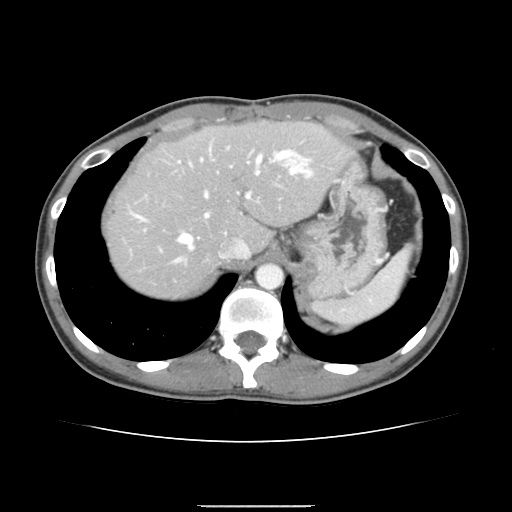
Contrast-enhanced abdominal CT, one axial slice. Slice 115 of 150 in the series (ordered by position). Intravenous contrast given. Soft-tissue window (W 400 / L 40 HU). 2.5 mm slice thickness. 512 × 512 image matrix. Female patient, age 32 years. Case-level facts recorded for this patient, not image findings: diagnosis: colorectal cancer liver metastases, imaged before liver resection; multiple liver metastases: yes; largest metastasis: 0.7 cm; disease in both lobes: no.
Structures marked on this image (outlined manually by an expert reader):
- hepatic veins: bounding box <134,151,297,264> (left, top, right, bottom; pixels)
- liver: <106,122,349,298>
- planned liver remnant (the part of the liver to remain after resection): <105,122,349,262>
- portal vein (with intrahepatic branches): <178,148,313,217>